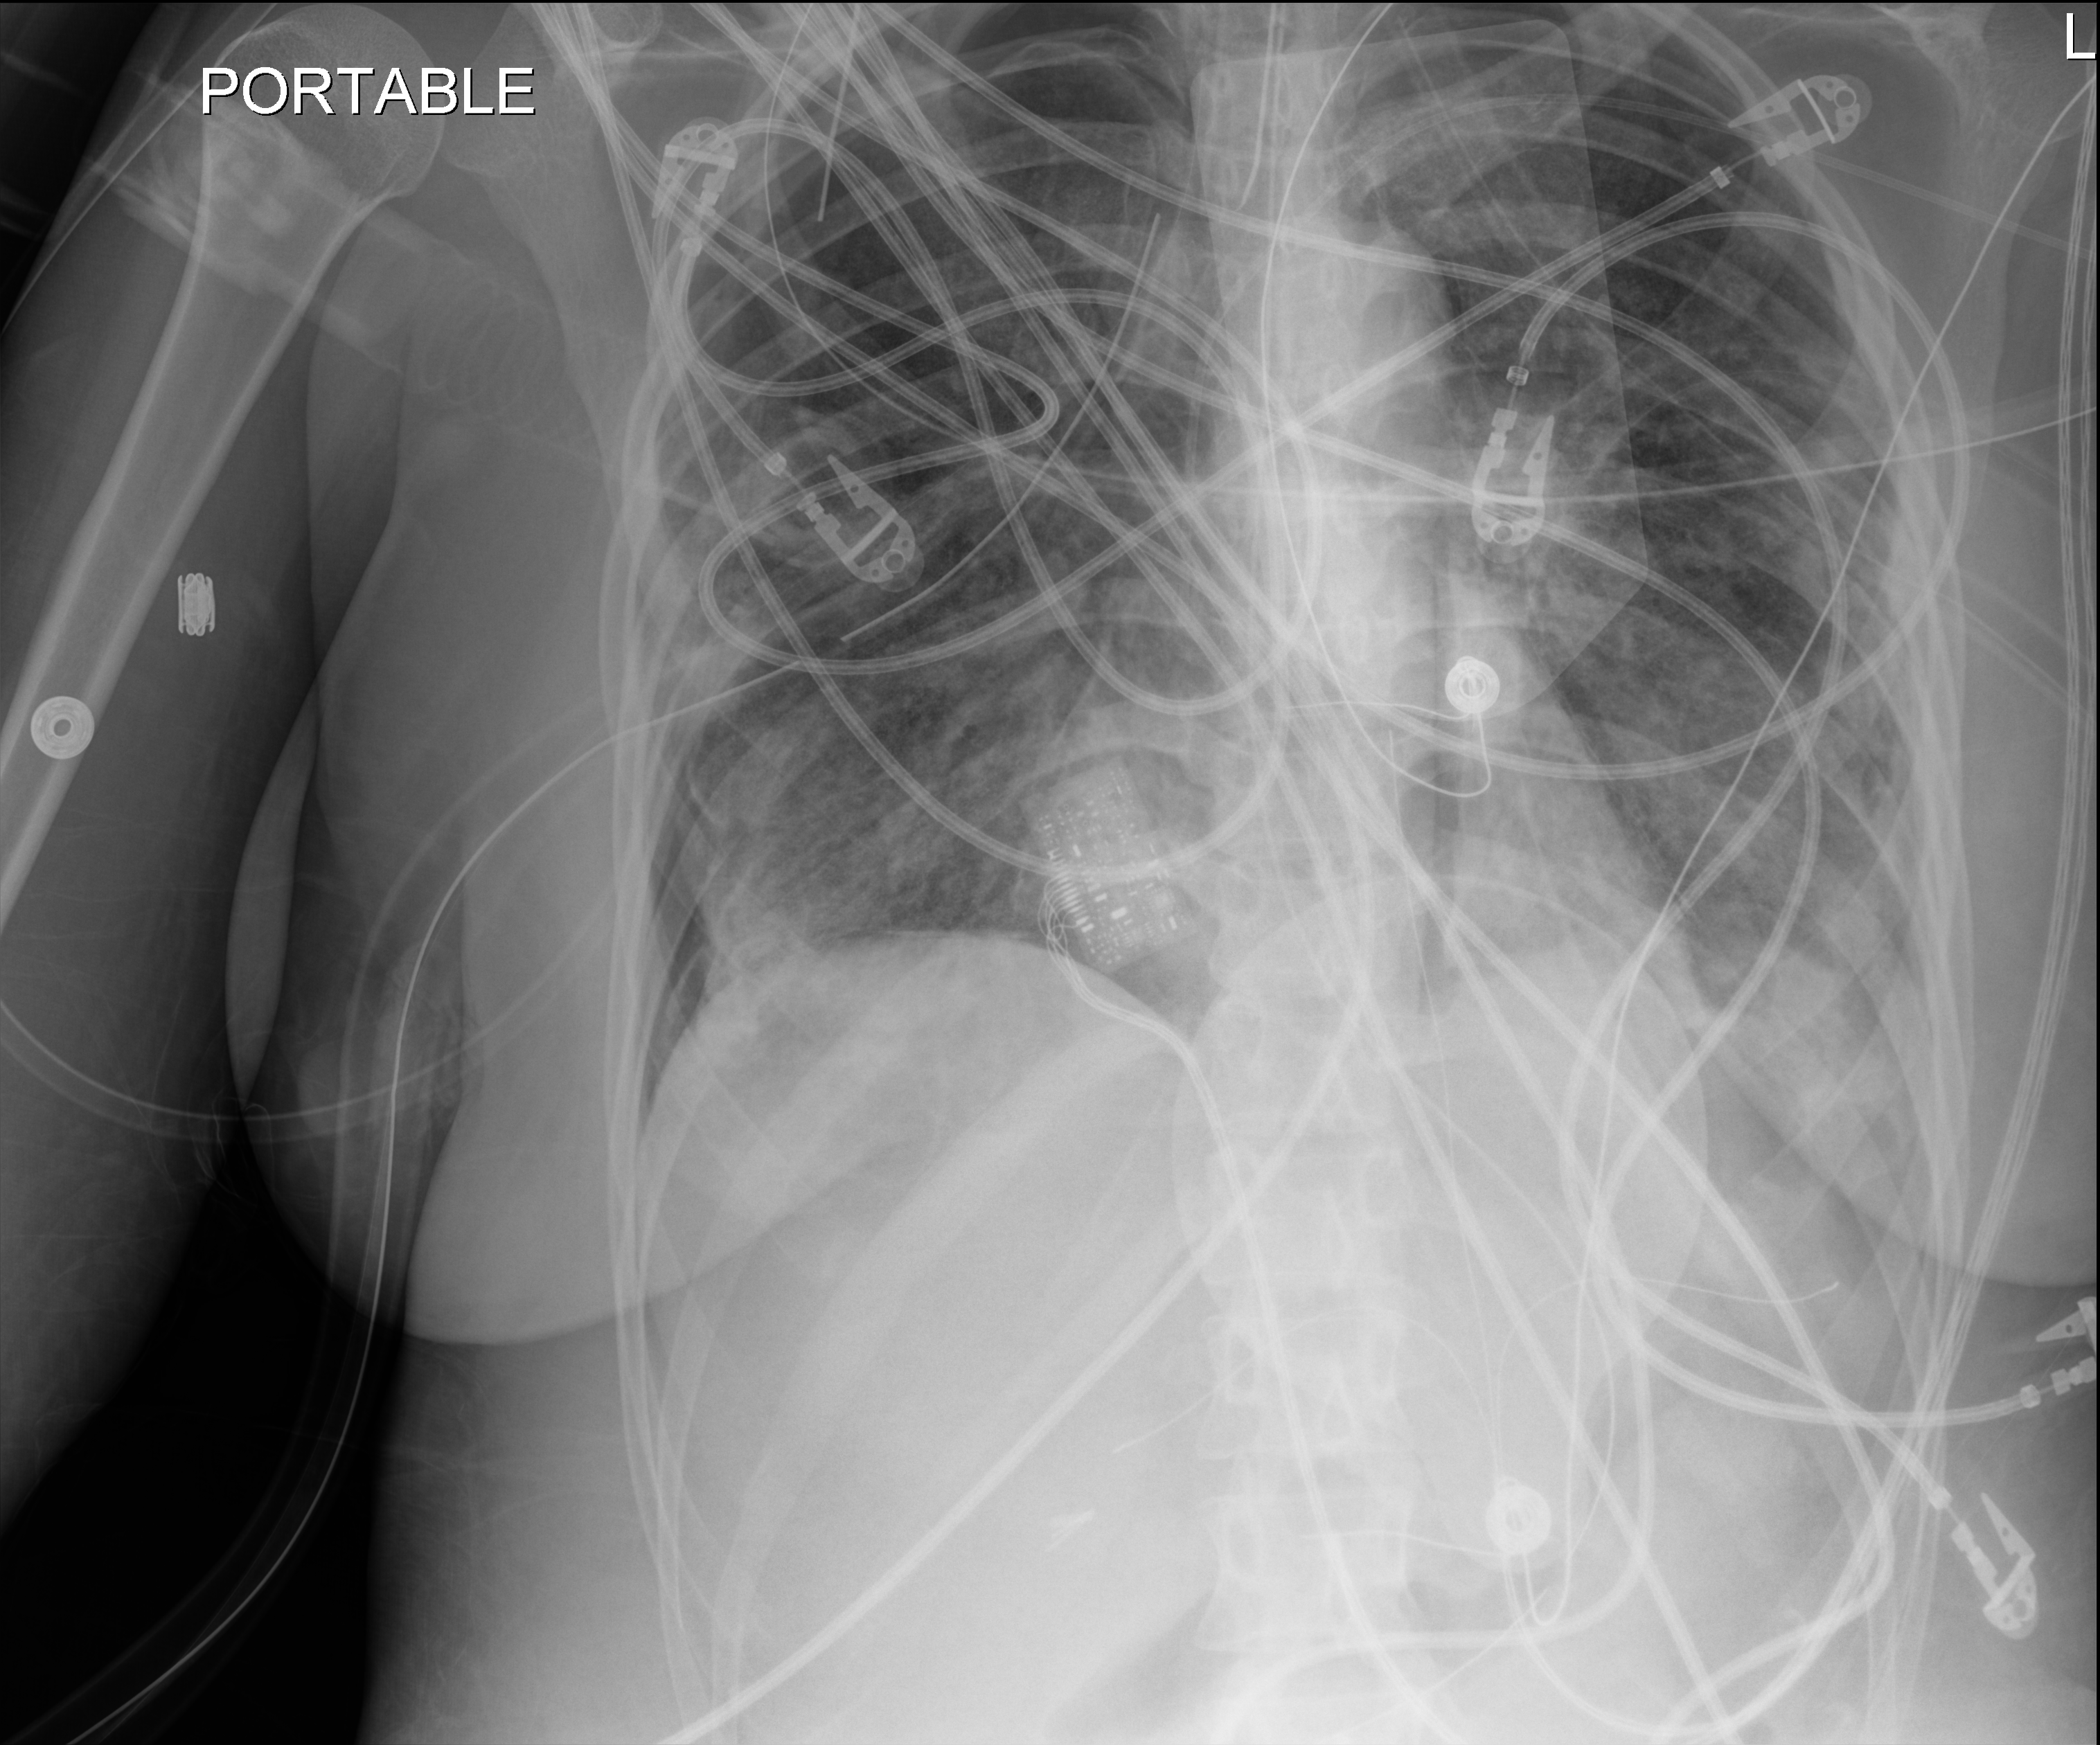
Chest X-ray (portable), anteroposterior (AP) projection. Adult patient hospitalised with COVID-19, age 18–59 years.
Admission-level facts for this patient (not findings on this image; timing relative to this image not recorded):
- mechanically ventilated during this hospital stay: yes